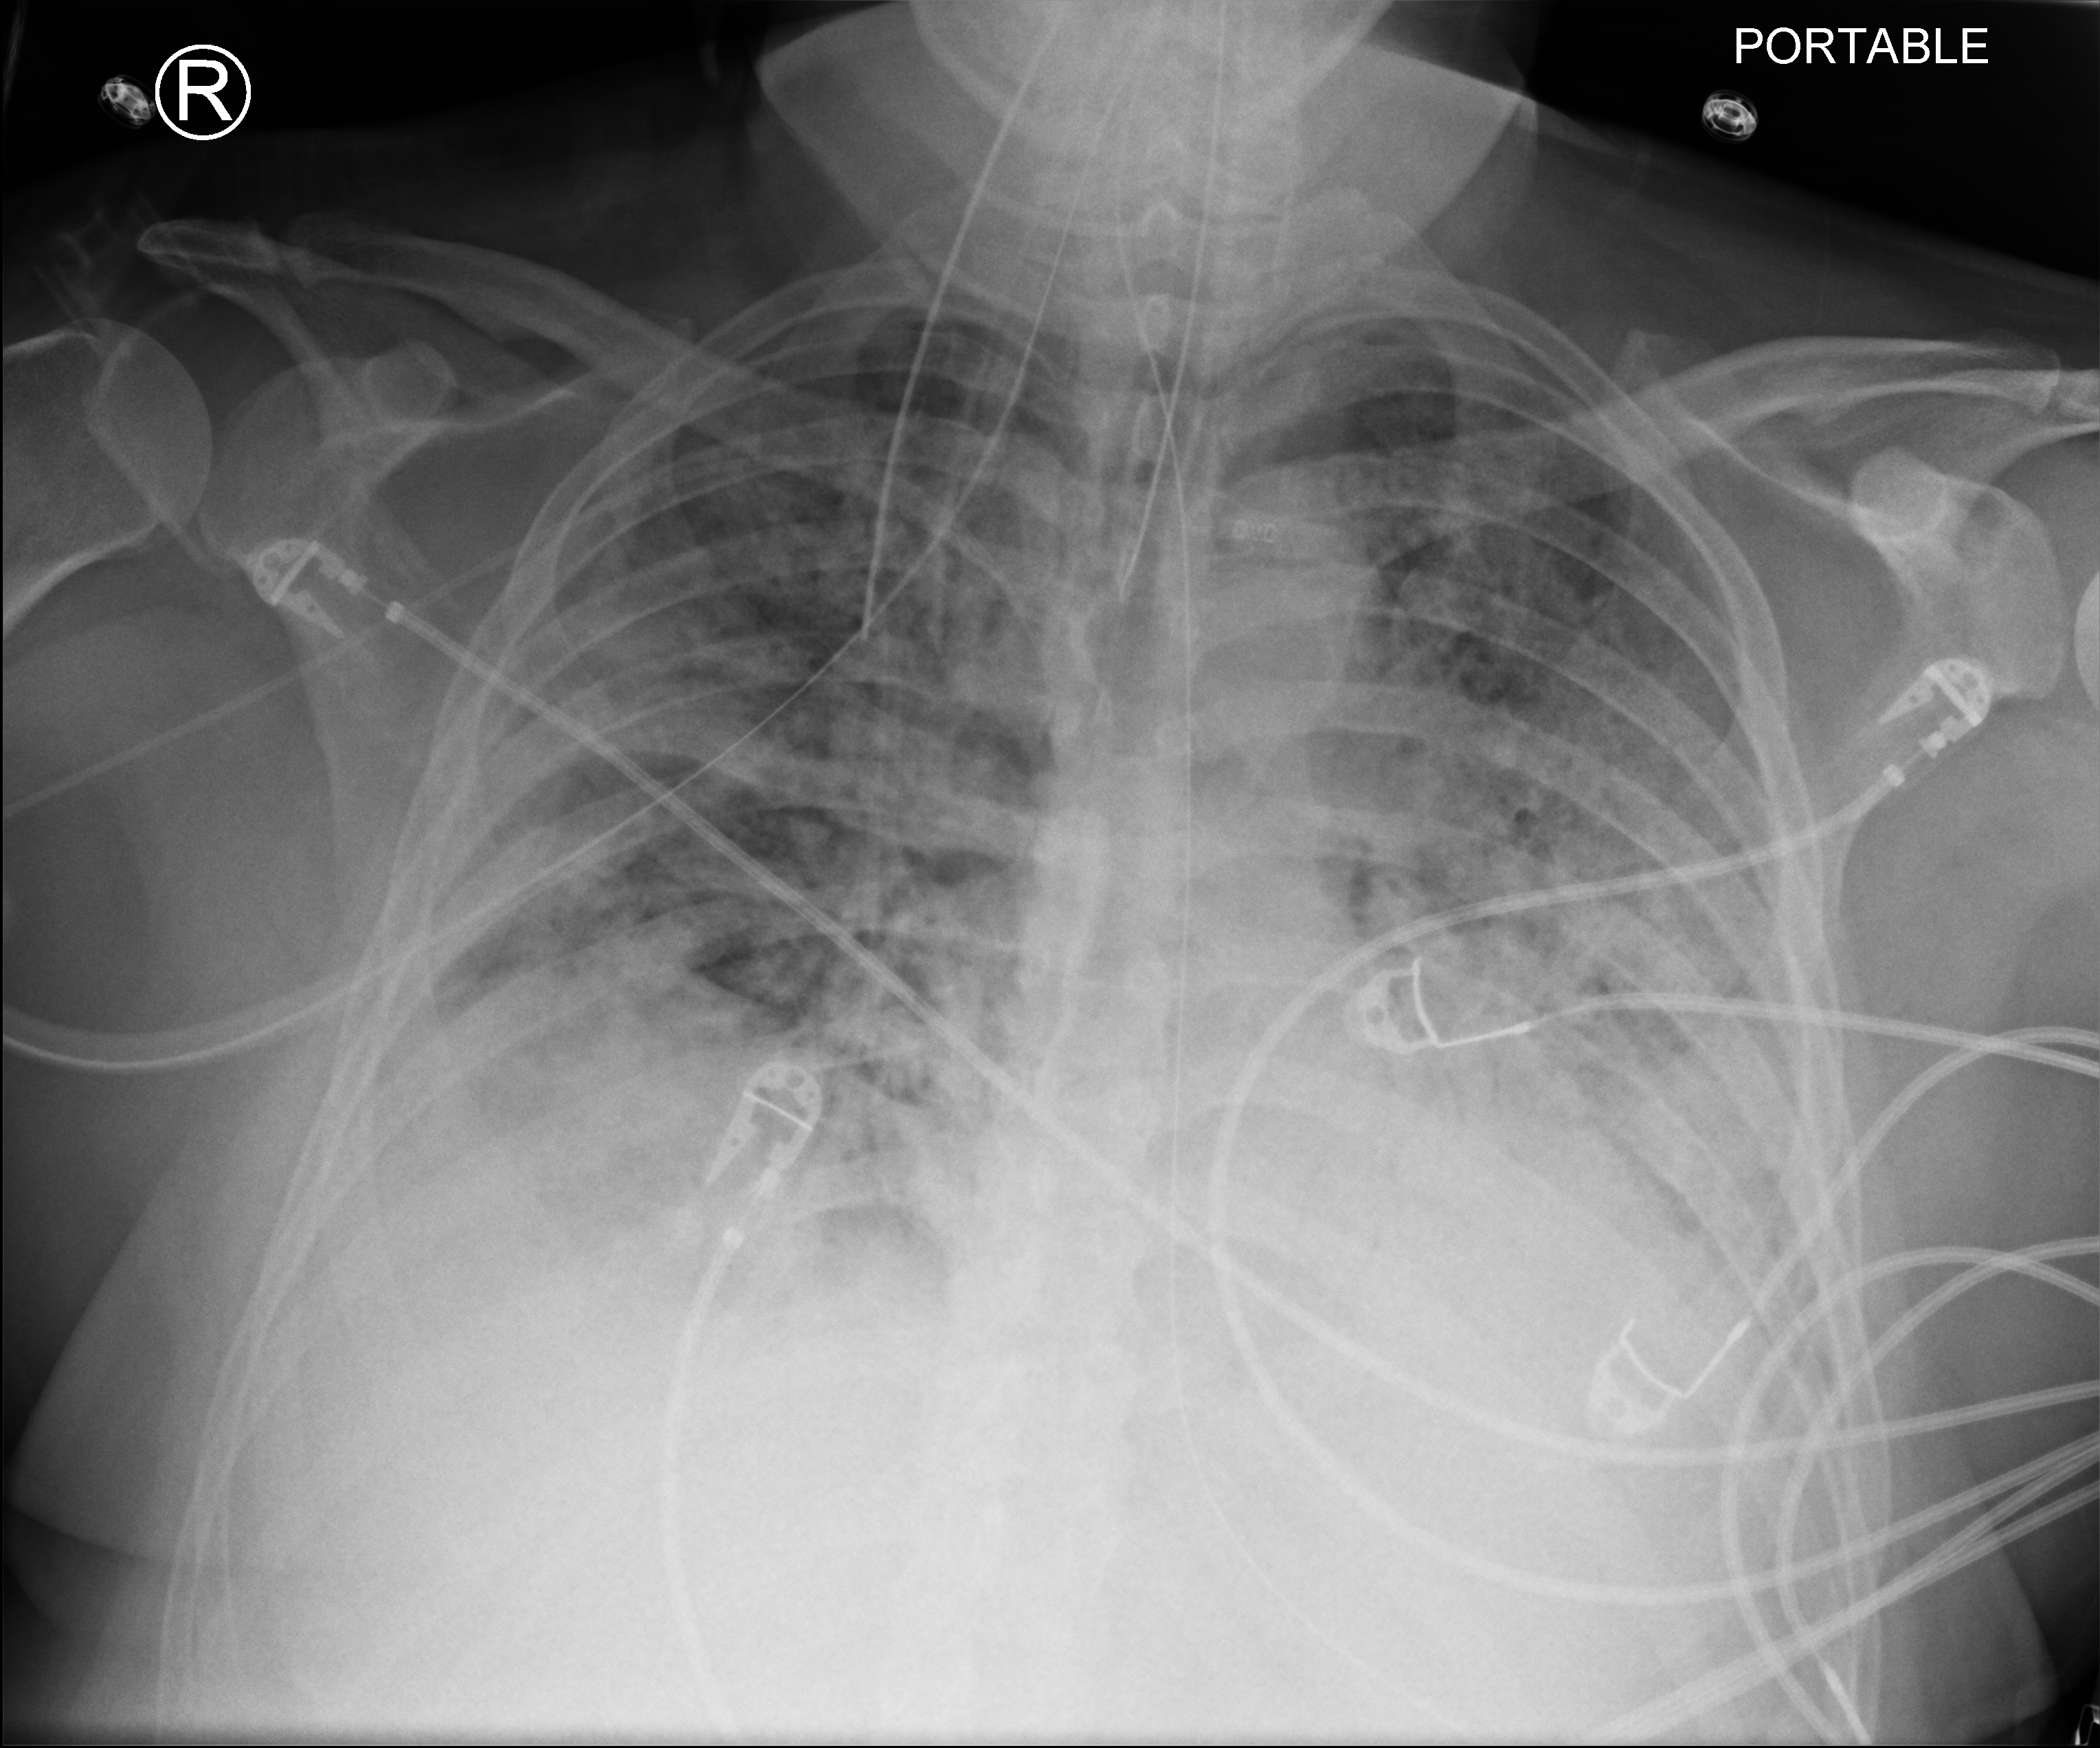
Chest X-ray (portable), anteroposterior (AP) projection. Patient hospitalised with COVID-19; male, aged 18–59 years.
From the hospital-stay record, not from the radiograph (when in the stay this image was taken is not recorded): length of hospital stay: 96 days.